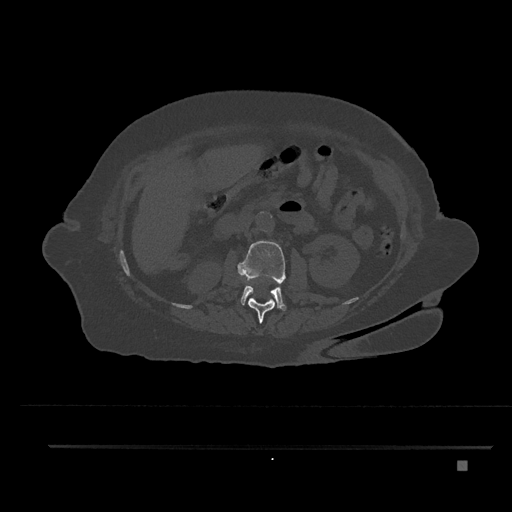
CT including the spine, one axial slice. Slice 199 of 797 in the series (ordered by position). 120 kVp. Bone window (W 1800 / L 400 HU). 512 × 512 image matrix. Female patient, age 76 years. Case-level facts recorded for this patient, not image findings: primary cancer: lung; vertebrae with lytic lesions (as recorded): T11, L3.
Annotated regions visible in this slice (semi-automatic segmentation, software-assisted and operator-edited):
- L1 vertebra: bounding box (x1, y1, x2, y2) in pixels: (248, 298, 276, 324)
- L2 vertebra: (237, 241, 286, 311)